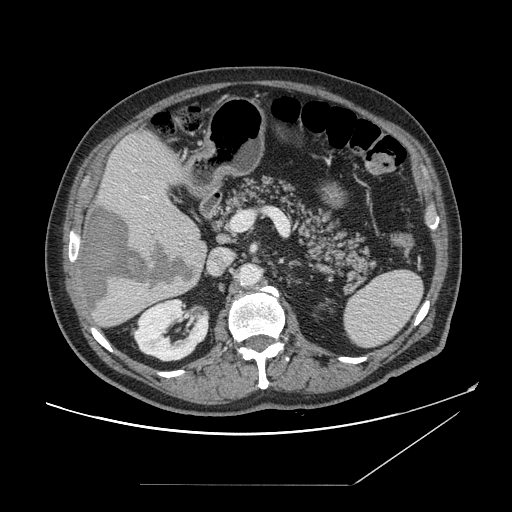
Contrast-enhanced abdominal CT, one axial slice. Position 82 of 166 along the scan axis. Intravenous contrast given. Soft-tissue window (W 400 / L 40 HU). 512 × 512 image matrix, field of view 416 × 416 mm. Male patient, age 80 years. From the clinical record (not read from this slice): diagnosis: colorectal cancer liver metastases, imaged before liver resection; multiple liver metastases: no; largest metastasis: 2.2 cm; disease in both lobes: no.
Annotated regions visible in this slice (expert manual segmentation):
- hepatic veins: bounding box [x1, y1, x2, y2] px = [145, 197, 148, 200]
- liver: [78, 131, 207, 328]
- planned liver remnant (the part of the liver to remain after resection): [101, 131, 200, 237]
- liver metastasis: [83, 206, 194, 309]